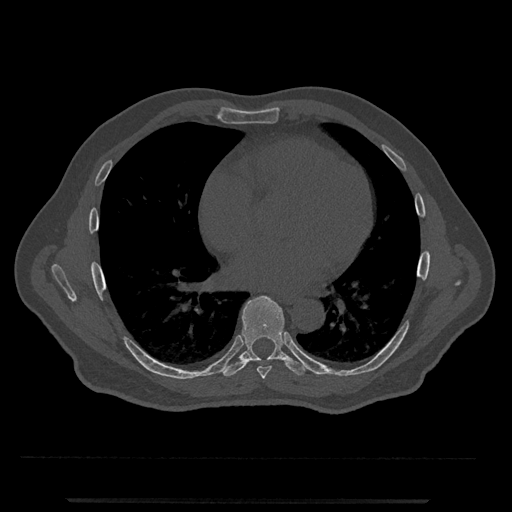
CT including the spine, one axial slice. Position 649 of 797 along the scan axis. Reconstruction kernel Br40s/3. 120 kVp. Bone window (W 1800 / L 400 HU). 0.5 mm slice thickness. 512 × 512 image matrix, field of view 419 × 419 mm. Male patient, age 63 years. From the clinical record (not read from this slice): primary cancer: prostate.
Outlined on this slice (semi-automatic segmentation, software-assisted and operator-edited):
- T7 vertebra: bounding box <257,366,272,379> (left, top, right, bottom; pixels)
- T8 vertebra: <223,296,307,377>